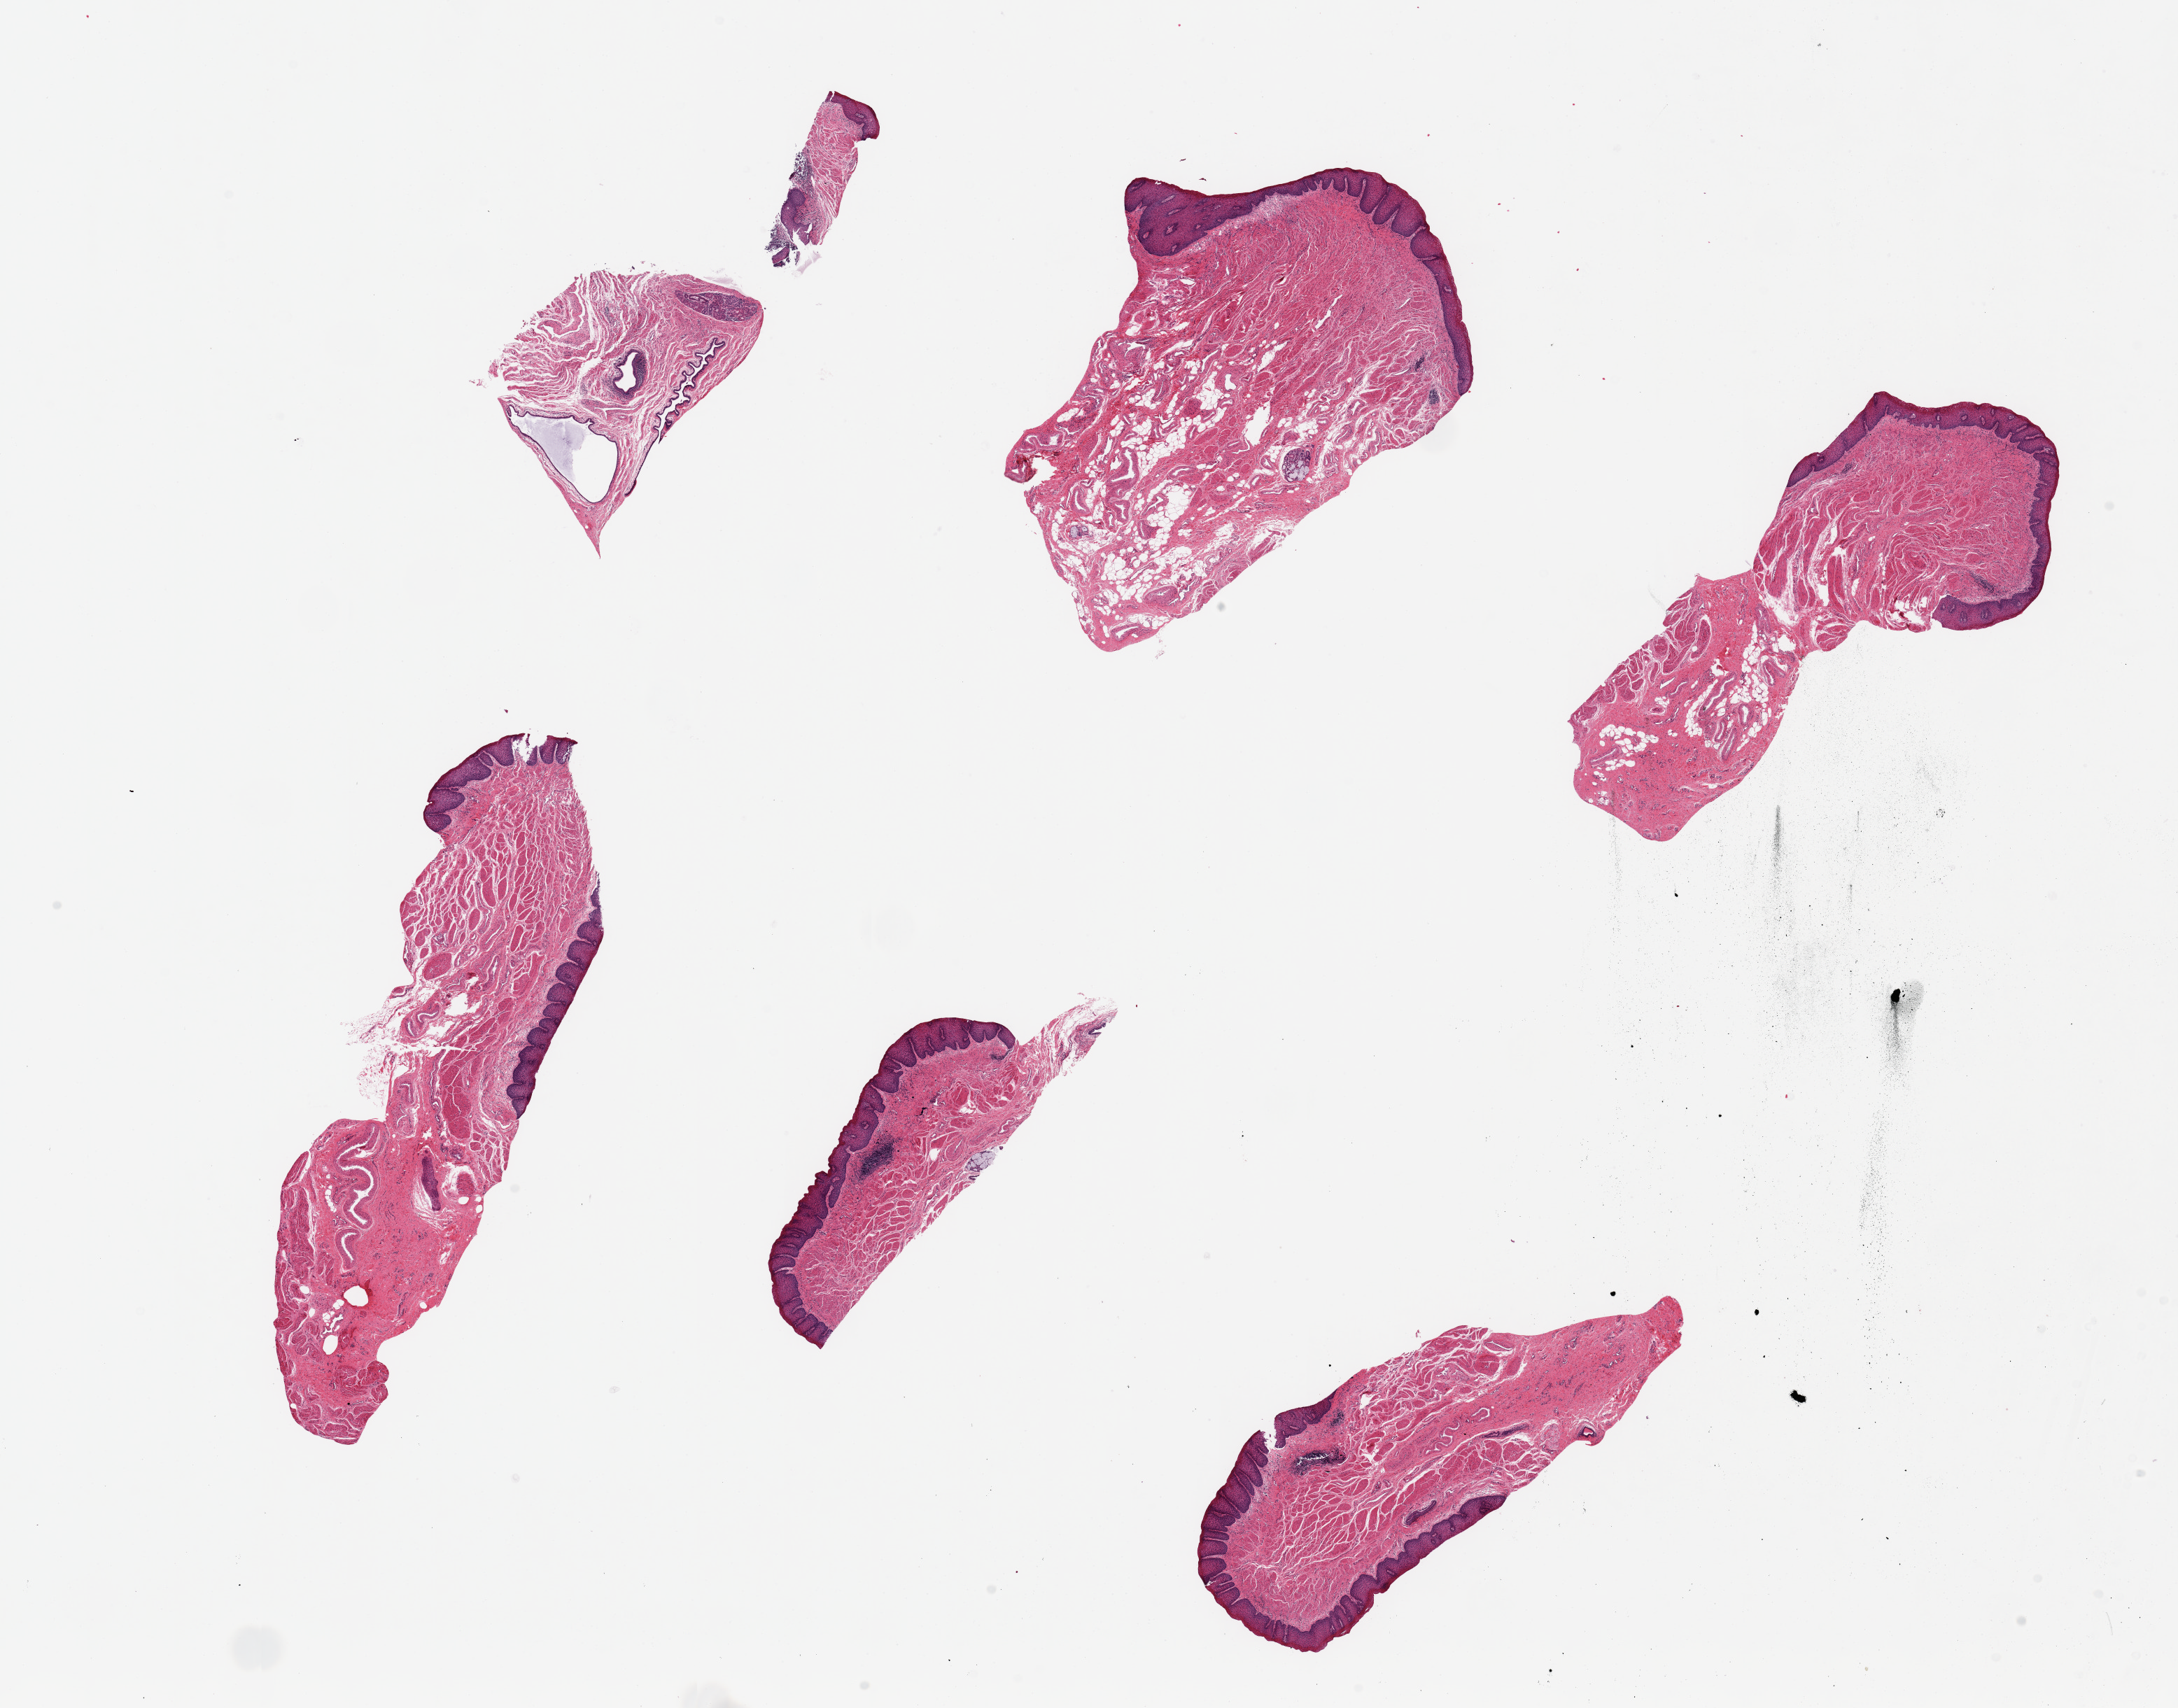
H&E whole-slide image, brightfield, low-resolution overview of the scanned area, about 24.6 x 19.3 mm; PAXgene-fixed paraffin-embedded (PFPE) section; target tissue: esophageal mucous membrane; donor tissue sample.
* reviewer comment on this tissue sample: 6 pieces ~7x2mm. Squamous mucosa up to 250 microns thick